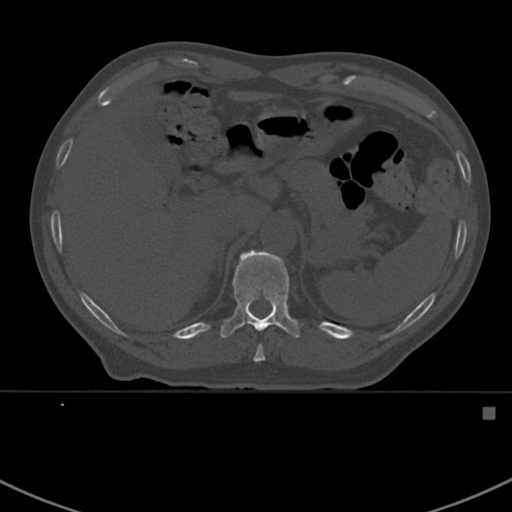
CT including the spine, one axial slice; slice 350 of 412 in the series (ordered by position); bone window (W 1800 / L 400 HU); 1.5 mm slice thickness; 512 × 512 image matrix, field of view 358 × 358 mm. Patient: male, 59 years. From the clinical record (not read from this slice): primary cancer: prostate.
Annotated regions visible in this slice (semi-automatic segmentation, software-assisted and operator-edited):
- T10 vertebra: bounding box [x1, y1, x2, y2] px = [253, 345, 265, 362]
- T11 vertebra: [220, 249, 304, 338]